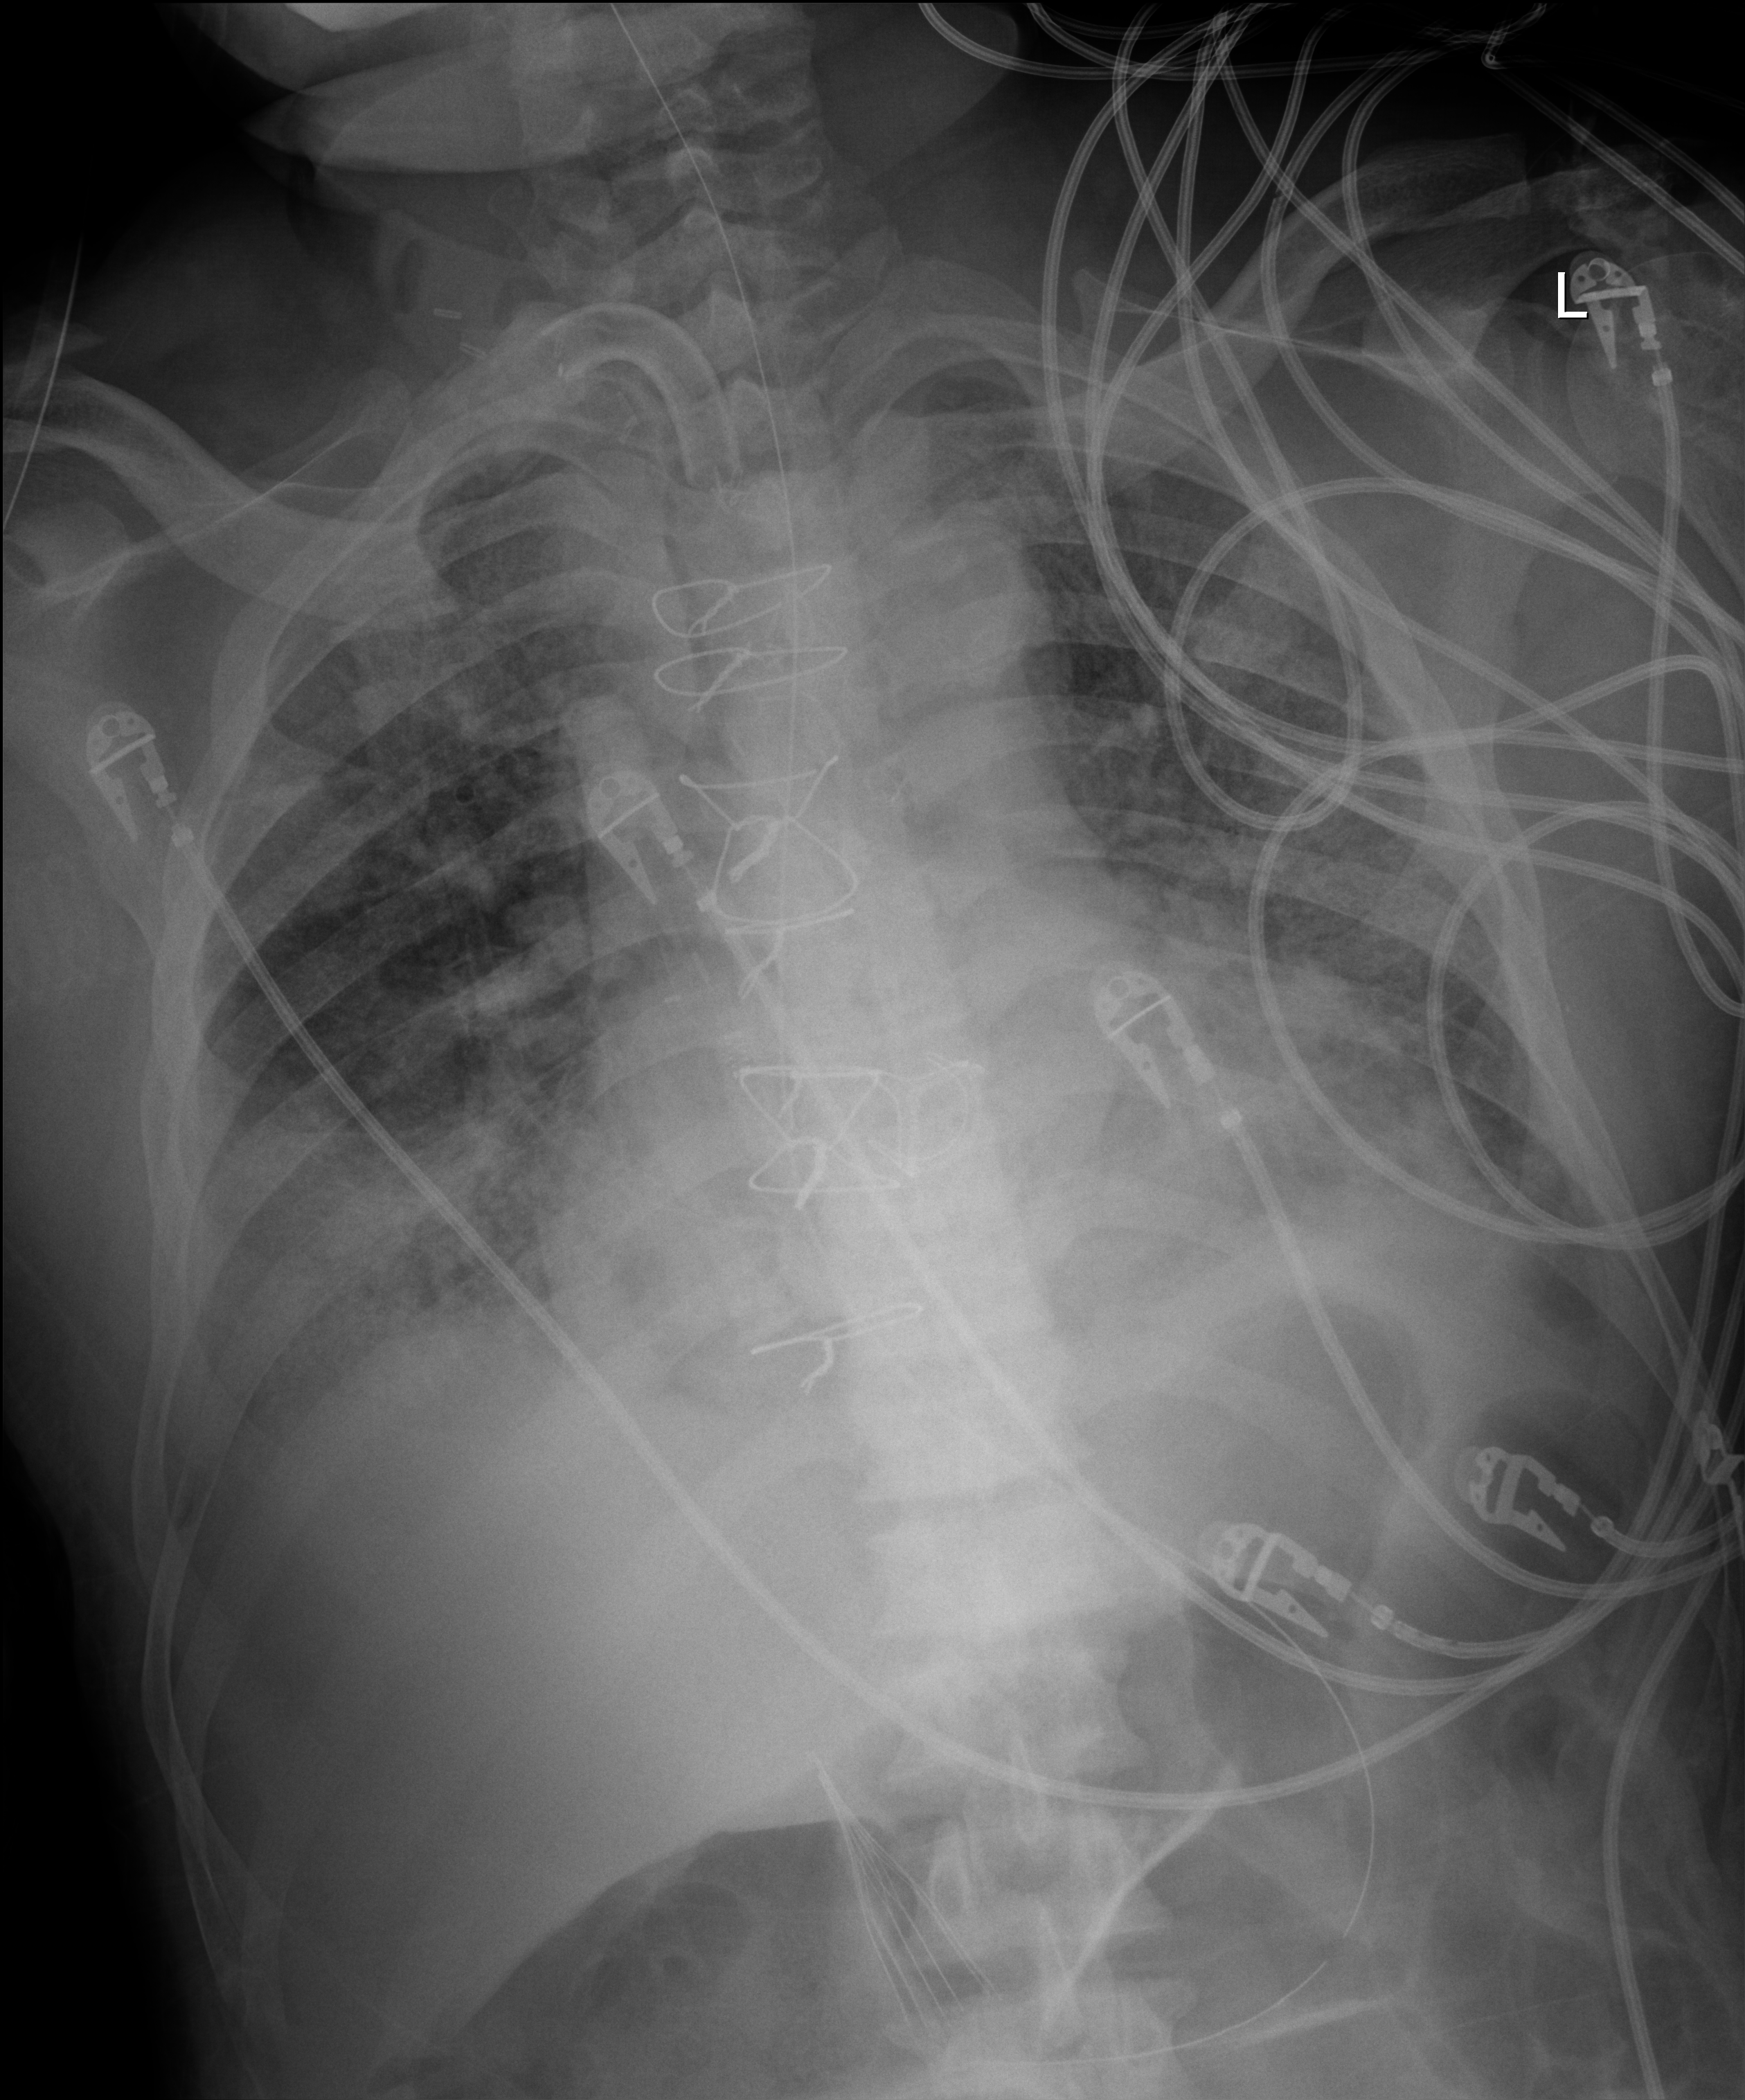
Chest X-ray (portable), anteroposterior (AP) projection. Patient hospitalised with COVID-19; male, aged 60–74 years.
Hospital-stay facts (about this admission, not read from this image; timing relative to this image not recorded):
- admitted to intensive care during this hospital stay: yes
- mechanically ventilated during this hospital stay: yes